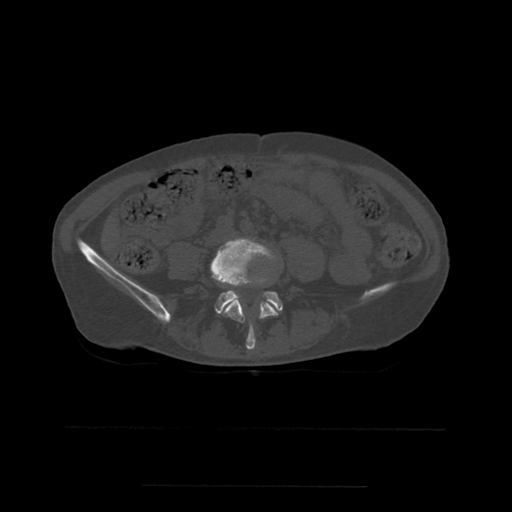
CT including the spine, one axial slice. Slice 157 of 544 in the series (ordered by position). Bone window (W 1800 / L 400 HU). 1.25 mm slice thickness. 512 × 512 image matrix, field of view 350 × 350 mm. Patient age 58 years. From the clinical record (not read from this slice): primary cancer: lung.
Annotated regions visible in this slice (semi-automatically segmented with operator editing):
- L4 vertebra: bounding box (x1, y1, x2, y2) in pixels: (212, 238, 279, 350)
- L5 vertebra: (211, 263, 283, 314)